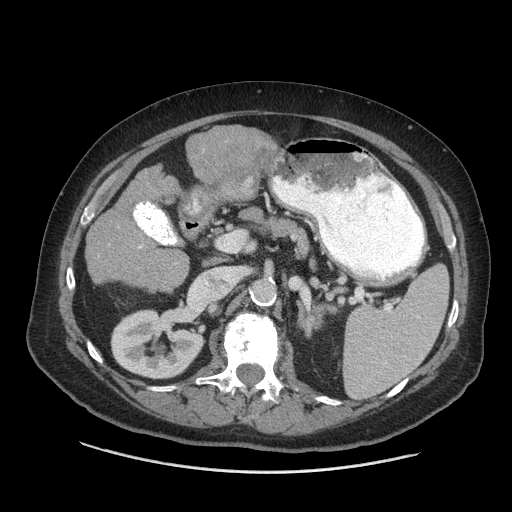
Contrast-enhanced abdominal CT (liver protocol), one axial slice. Slice 28 of 77 in the series (ordered by position). Reconstruction kernel STANDARD. 140 kVp. Soft-tissue window (W 400 / L 40 HU). 2.5 mm slice thickness. 512 × 512 image matrix, field of view 420 × 420 mm. Case-level facts recorded for this patient, not image findings: diagnosis: hepatocellular carcinoma (patient treated with transarterial chemoembolisation; whether this scan precedes or follows treatment is not stated here); TNM stage (as recorded): Stage-I; Child-Pugh class: A; tumour differentiation: well differentiated; tumour size: 3.8 cm.
Structures marked on this image (semi-automatically segmented with operator editing):
- liver parenchyma outside the tumour (the mass and vessels are separate outlines, so this box may not span the whole liver): bounding box [x1, y1, x2, y2] px = [89, 126, 271, 284]